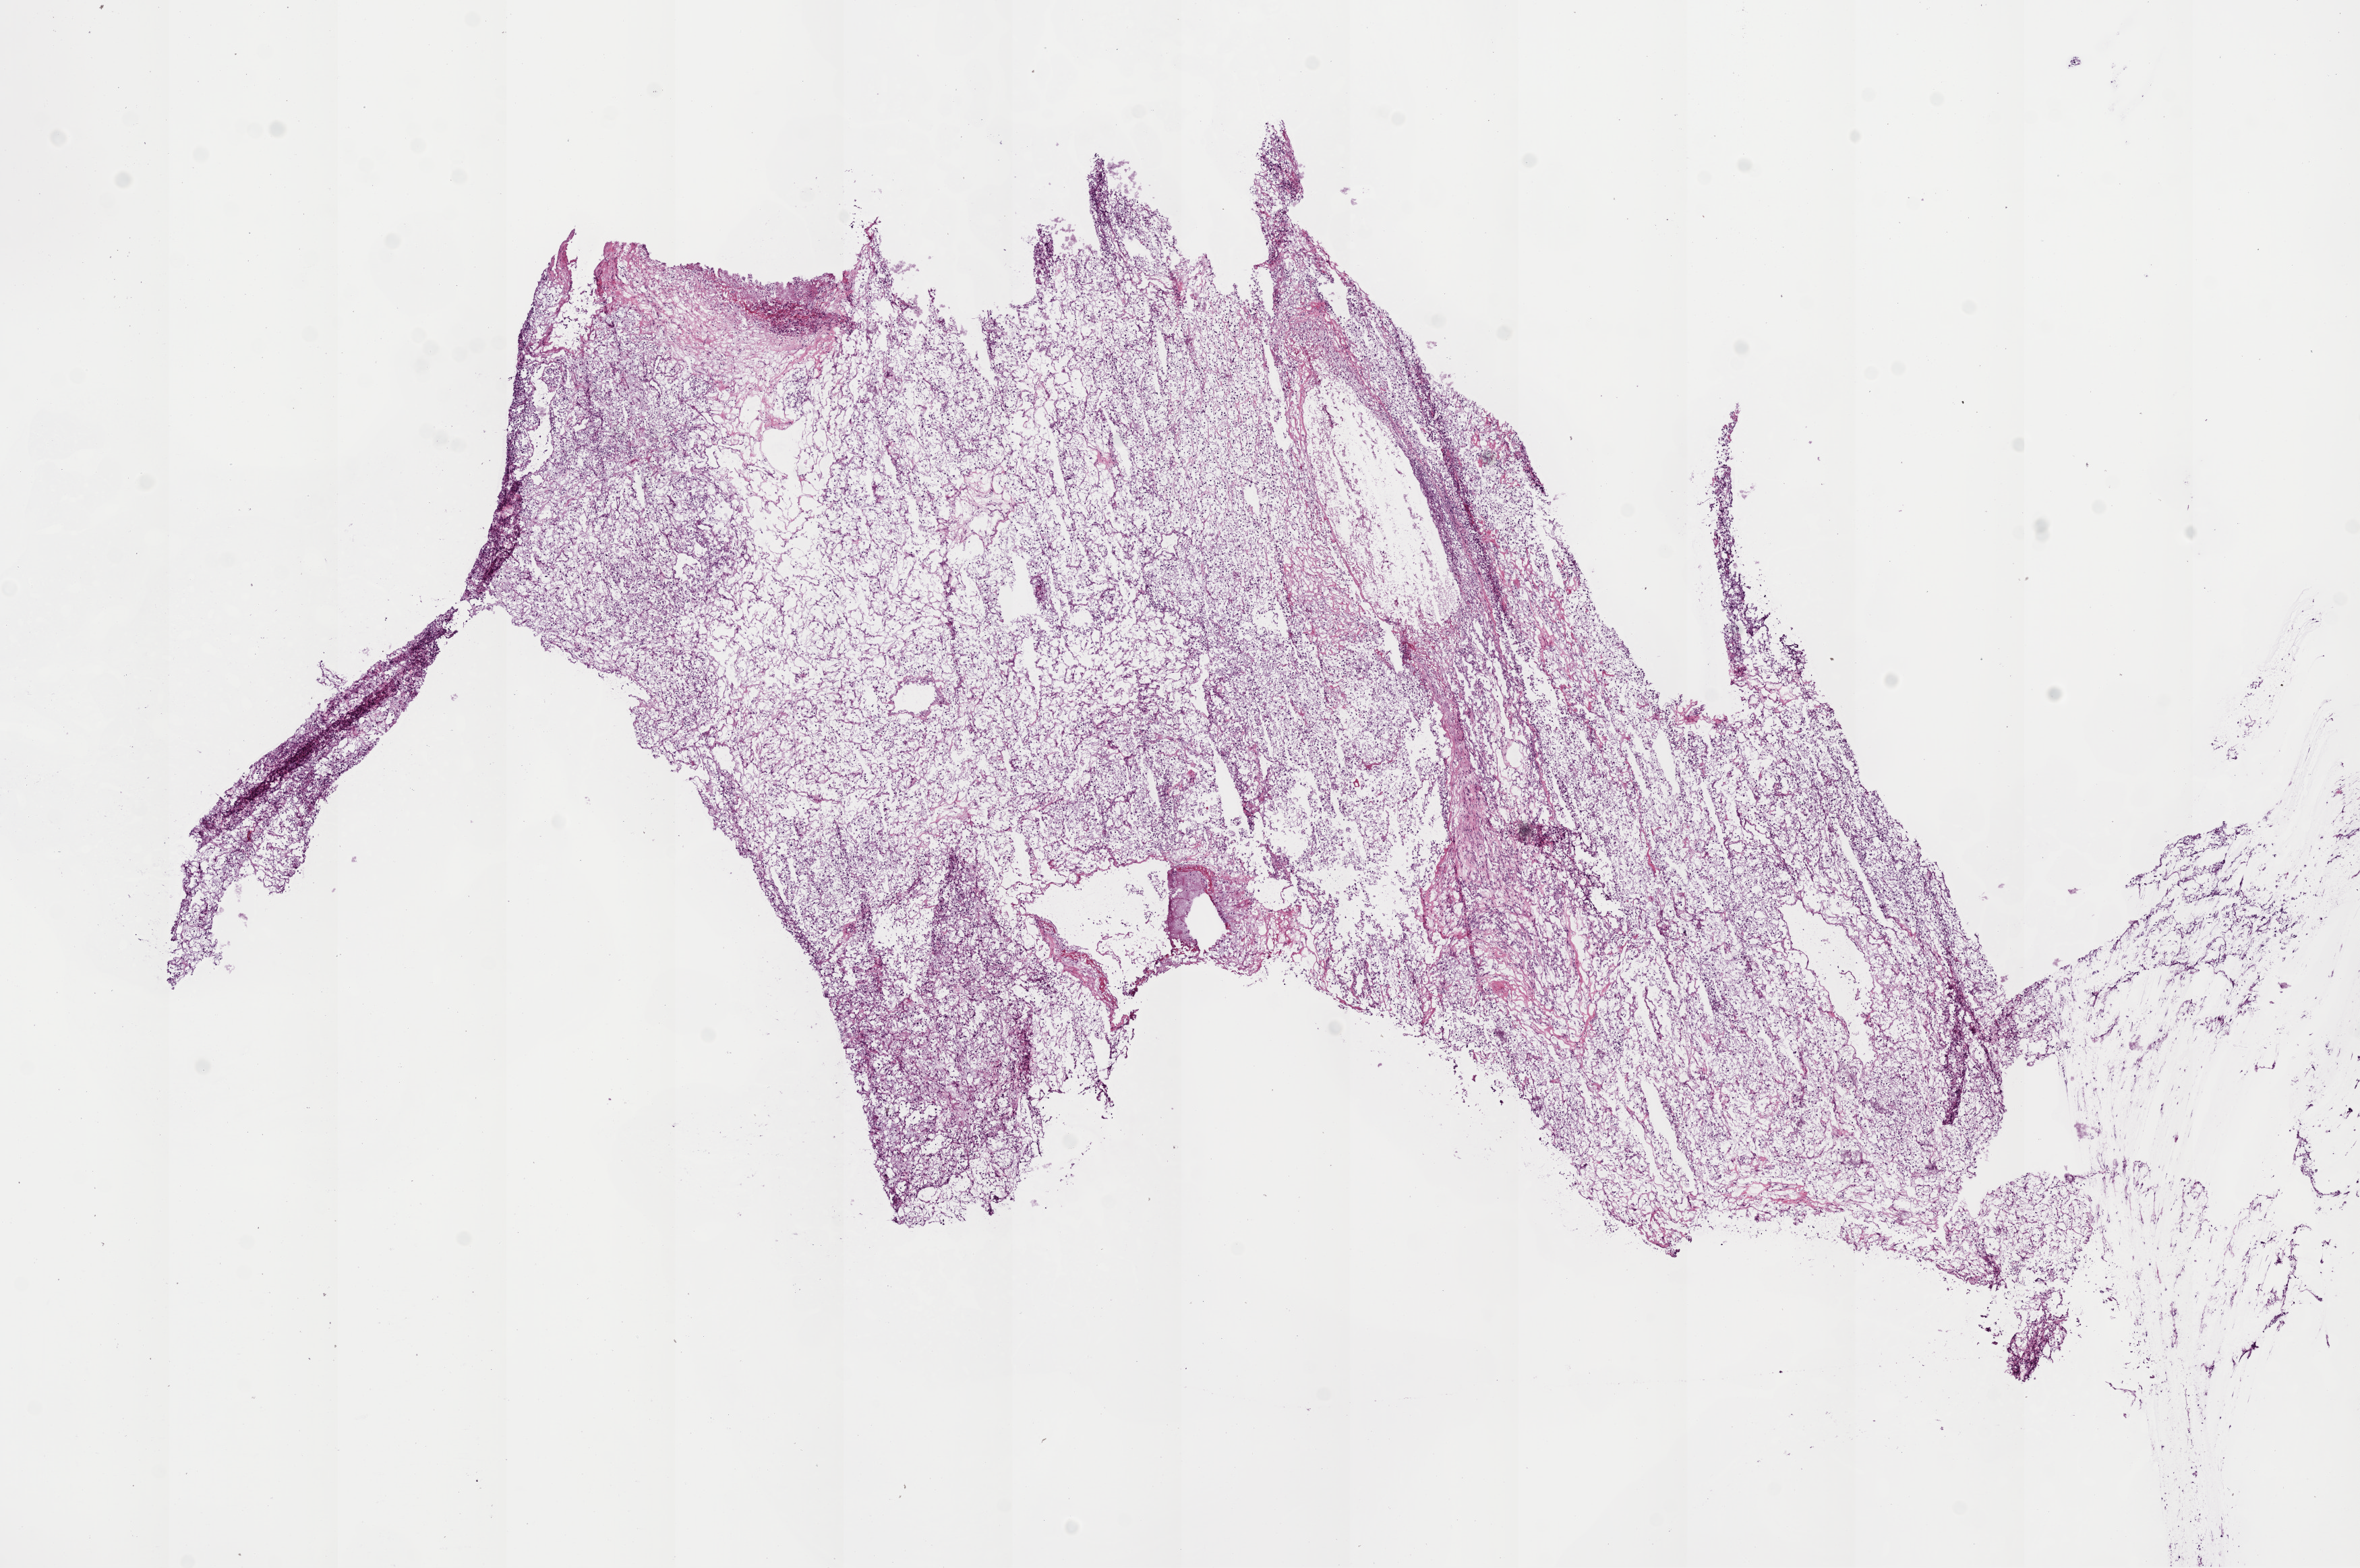
Whole-slide histology image, Hematoxylin and eosin (H&E) stained, whole scanned area (about 14.0 x 9.3 mm, slide scanned at 20x) shown as a low-resolution overview. Frozen section. Primary tumour sample from the kidney. Male patient; age at initial diagnosis 26 years. Histologic grade: G2 (moderately differentiated). Slide review estimates, as recorded: tumour cells 90%, tumour nuclei 85%, normal cells 0%, stromal cells 10%, necrosis 0%.
AJCC pathologic stage: I. TNM: T1a NX M0. Histologic diagnosis: Clear cell adenocarcinoma, NOS.